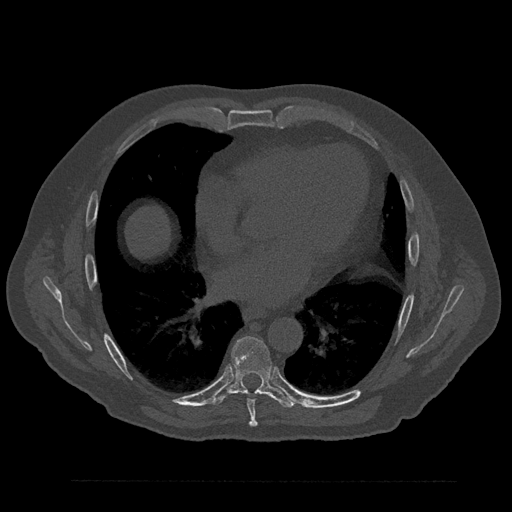
CT including the spine, one axial slice. Bone window (W 1800 / L 400 HU). 0.5 mm slice thickness. 512 × 512 image matrix, field of view 430 × 430 mm. Male patient, age 61 years. From the clinical record (not read from this slice): primary cancer: prostate.
Annotated regions visible in this slice (semi-automatic segmentation, software-assisted and operator-edited):
- T7 vertebra: bounding box <242,391,258,427> (left, top, right, bottom; pixels)
- T8 vertebra: <213,336,296,408>